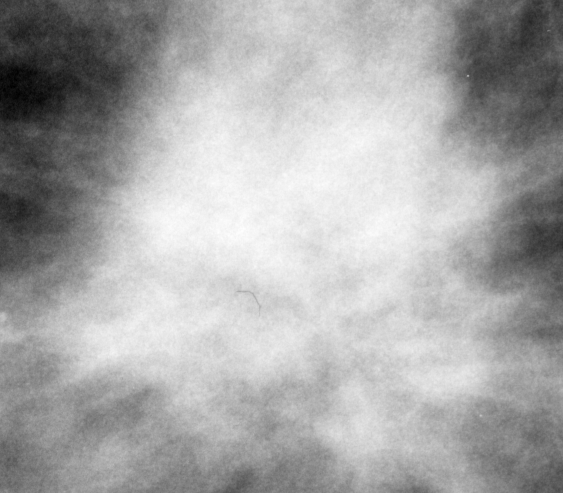
Region of interest cut from a scanned film mammogram (one marked finding), left breast, MLO view.
Finding: mass, shape irregular, margins spiculated; BI-RADS assessment category 5; subtlety rating 5 on a 1 (subtle) to 5 (obvious) scale; pathology result (as recorded, not read from the image): malignant.